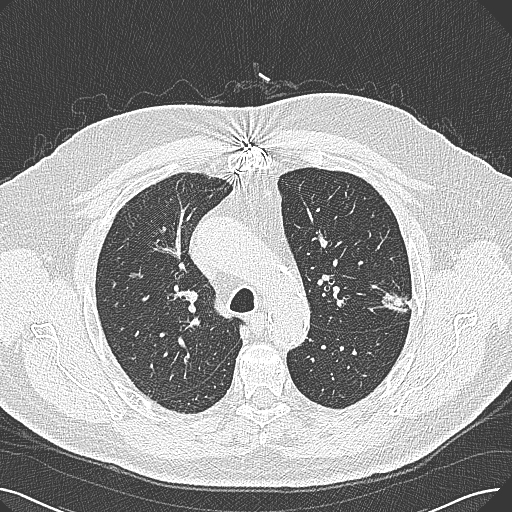
Low-dose screening chest CT, axial slice, baseline annual screen, lung window (W 1500 / L -600 HU), 1 mm slice thickness, lung (sharp) reconstruction kernel (B80f). Male, age 74 years at enrolment. Former smoker at enrolment.
Lesion marked by an expert reader, box from (x=371, y=273) to (x=425, y=321) px. The exam's reader record, not a measurement of the box and not confirmed to be the same lesion: non-calcified nodule or mass ≥4 mm, left upper lobe, 15 × 10 mm, poorly defined margins, soft tissue attenuation. Official screen result: positive, change unspecified: nodule(s) >= 4 mm or enlarging nodule(s), mass(es), or other non-specific abnormalities suspicious for lung cancer. Participant outcome: lung cancer diagnosed 124 days after this screen — adenocarcinoma, NOS, left upper lobe, well differentiated (G1), stage IA (AJCC 6th edition), 26 mm at pathology.